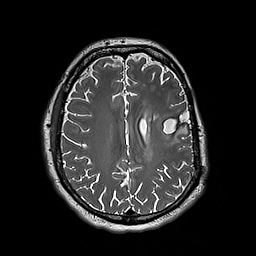
Brain MRI from a brain-tumour surgery series, one axial slice; slice 77 of 192 in the series (ordered by position); 256 × 256 image matrix, field of view 250 × 250 mm. From the clinical record (not read from this slice): histopathology: Astrocytoma; WHO grade: 3; IDH mutation: yes; tumour location: Left Insular.
Annotated regions visible in this slice (manually delineated by an expert):
- tumour: box from (x=153, y=114) to (x=170, y=137) px